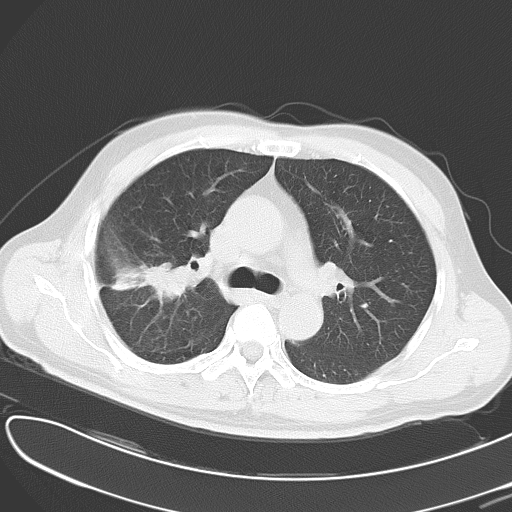
Chest CT, one axial slice; slice 32 of 49 in the series (ordered by position); 120 kVp; lung window (W 1500 / L -600 HU); 6 mm slice thickness; 512 × 512 image matrix, field of view 353 × 353 mm. Male patient, age 53 years. Case-level facts recorded for this patient, not image findings: clinical TNM (as recorded): T2 N1 M0.
Outlined on this slice (bounding box drawn by a radiologist):
- lung tumour (recorded histology: adenocarcinoma): bounding box (x1, y1, x2, y2) in pixels: (101, 253, 194, 301)